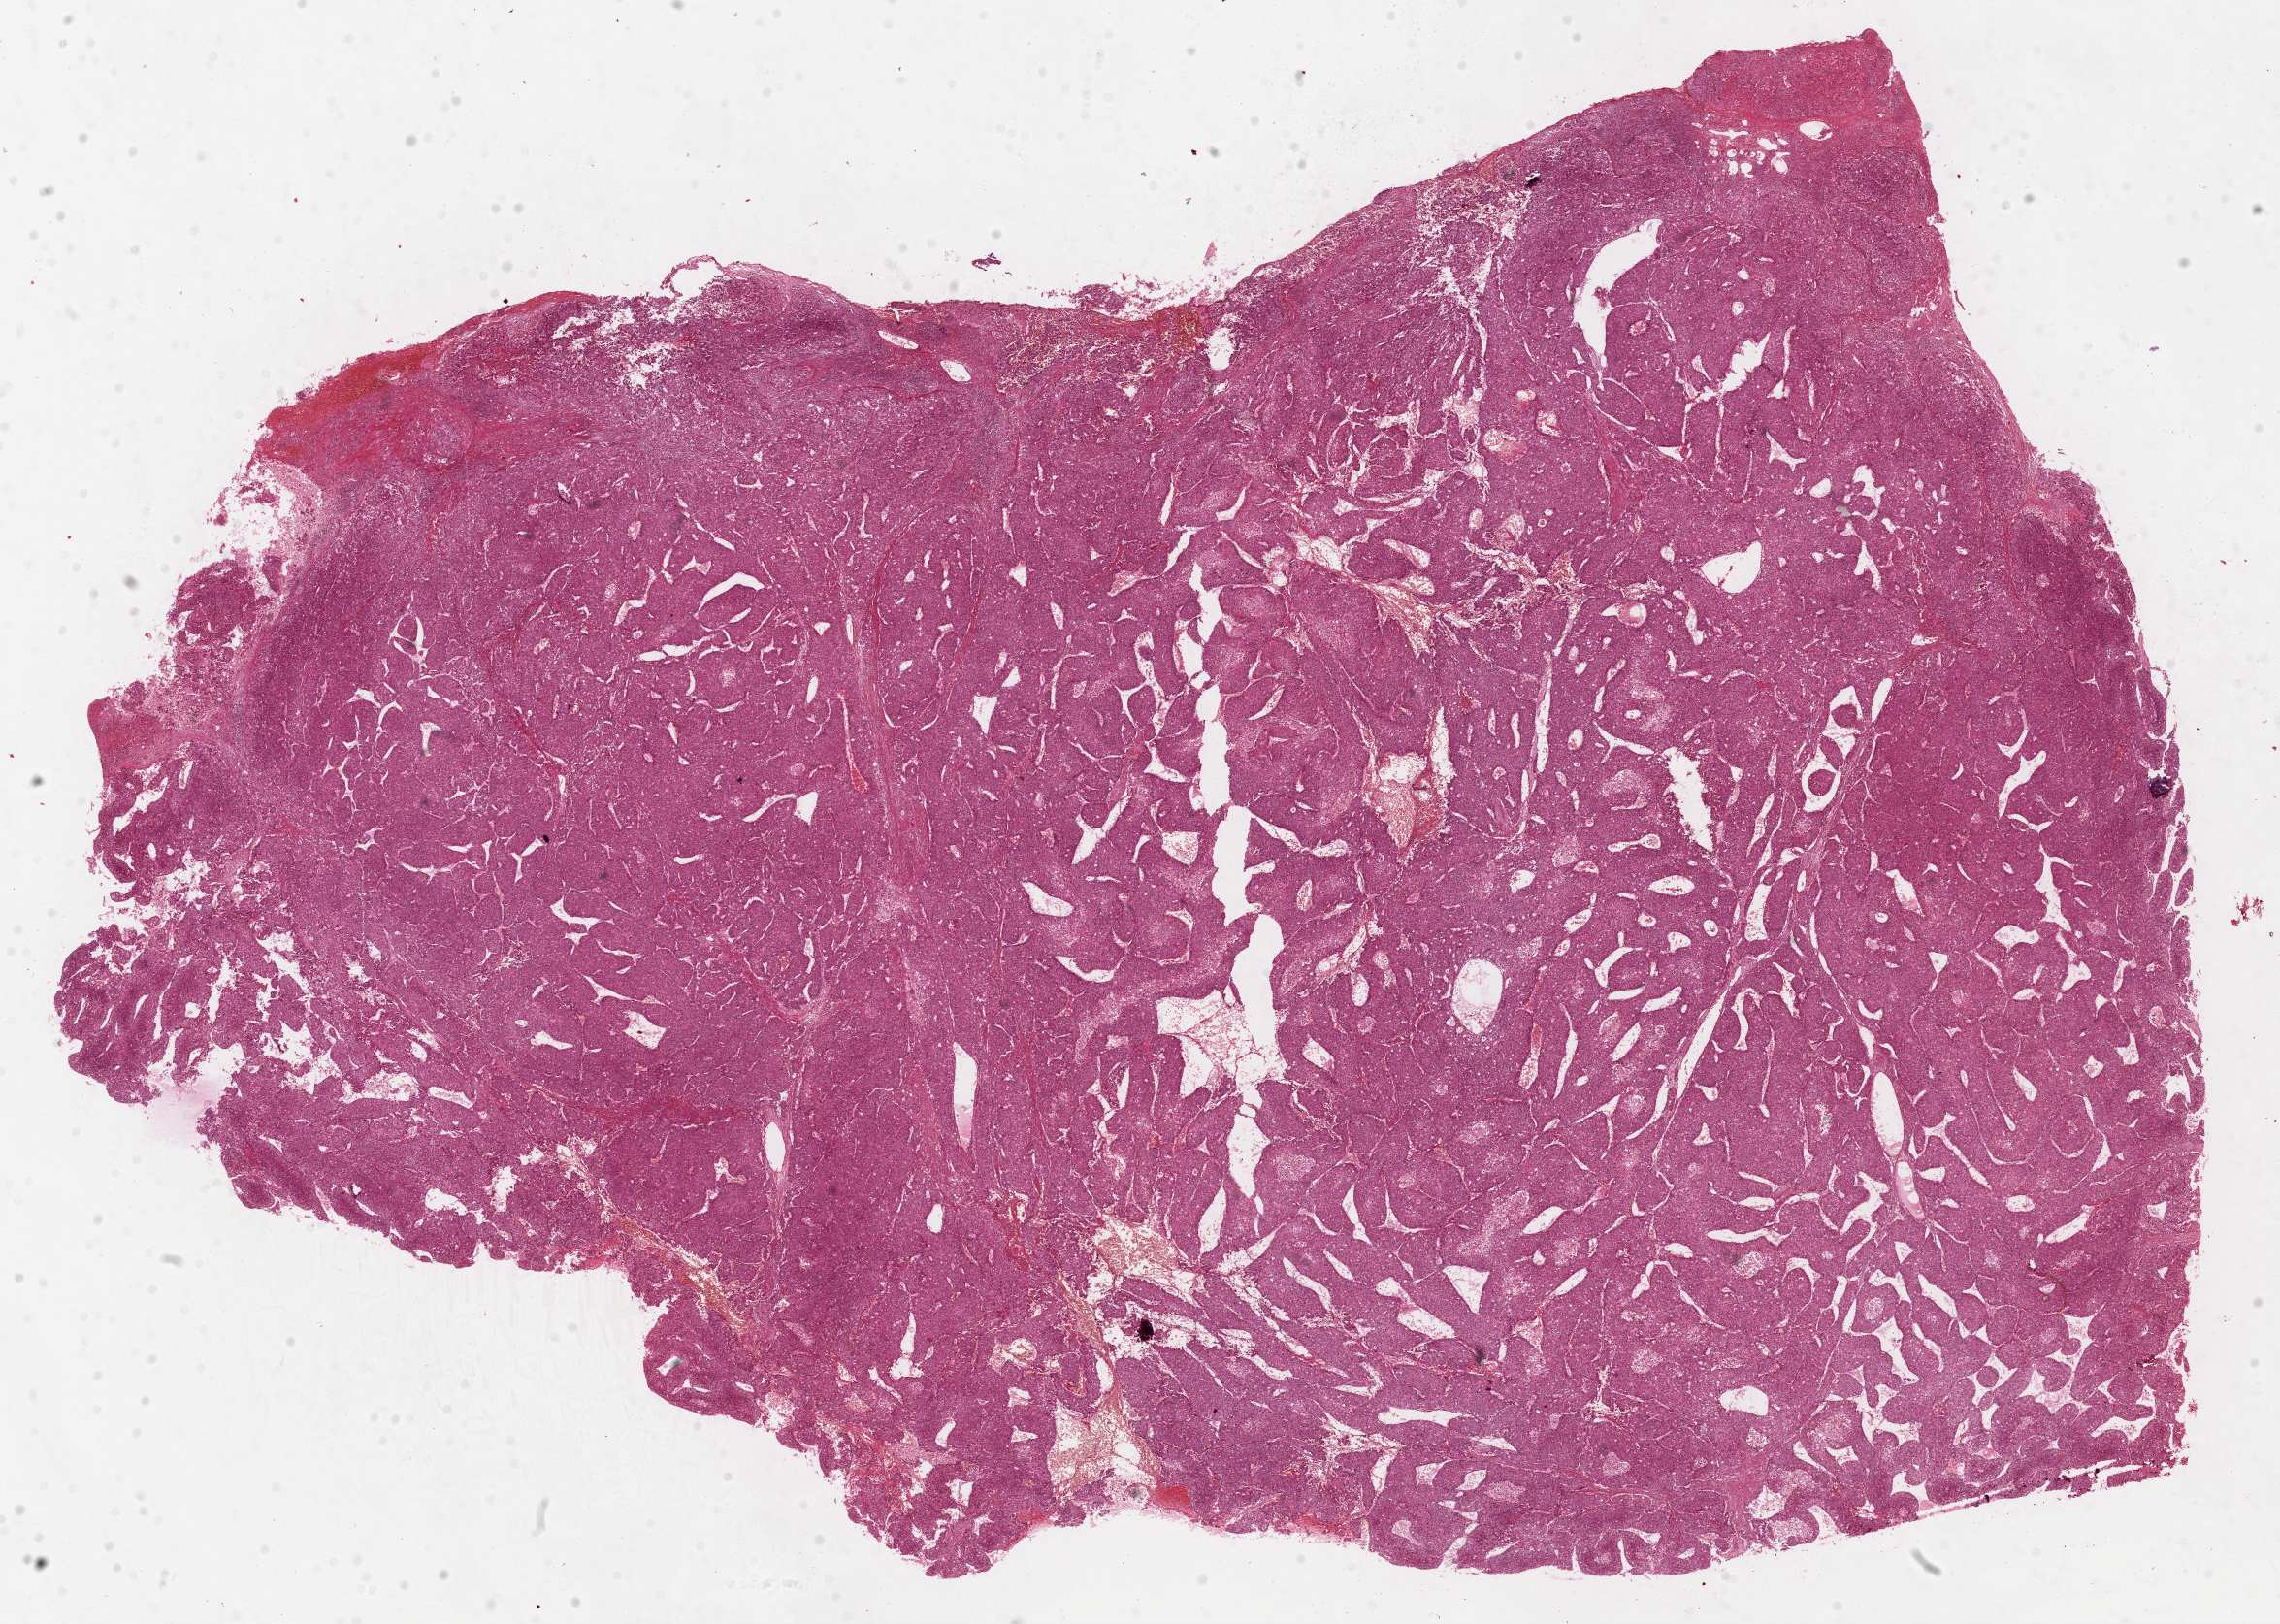
Digitized H&E tissue section (whole slide) — shown as a low-resolution overview of the whole scanned area (about 18.6 x 13.2 mm, acquisition: 40x scan); FFPE section; sample: primary tumour, liver. Patient: male, age at initial diagnosis 71 years.
Diagnosis: Hepatocellular carcinoma, NOS.